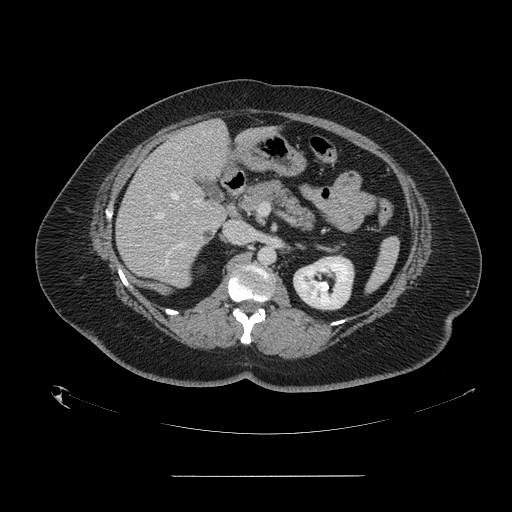
Contrast-enhanced abdominal CT, one axial slice; slice 79 of 164 in the series (ordered by position); 120 kVp; intravenous contrast given; soft-tissue window (W 400 / L 40 HU); 2.5 mm slice thickness; 512 × 512 image matrix. Female patient, age 52 years. From the clinical record (not read from this slice): diagnosis: colorectal cancer liver metastases, imaged before liver resection; multiple liver metastases: yes; largest metastasis: 3.5 cm; disease in both lobes: no.
Annotated regions visible in this slice (outlined manually by an expert reader):
- hepatic veins: box from (x=155, y=132) to (x=203, y=219) px
- liver: (x=117, y=121)–(x=228, y=286)
- planned liver remnant (the part of the liver to remain after resection): (x=177, y=121)–(x=227, y=175)
- portal vein (with intrahepatic branches): (x=163, y=200)–(x=199, y=237)
- liver metastasis: (x=204, y=231)–(x=214, y=243)